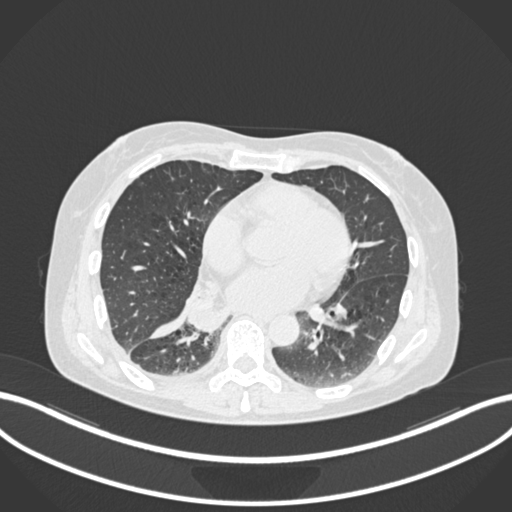
Chest CT, one axial slice; position 67 of 168 along the scan axis; reconstruction kernel B30f; lung window (W 1500 / L -600 HU); 1 mm slice thickness; 512 × 512 image matrix, field of view 400 × 400 mm. Female patient, age 63 years. From the clinical record (not read from this slice): clinical TNM (as recorded): T1c N0 M0.
Annotated regions visible in this slice (rectangle marked by the reading radiologist):
- lung tumour (recorded histology: adenocarcinoma): bounding box (x1, y1, x2, y2) in pixels: (180, 286, 237, 334)